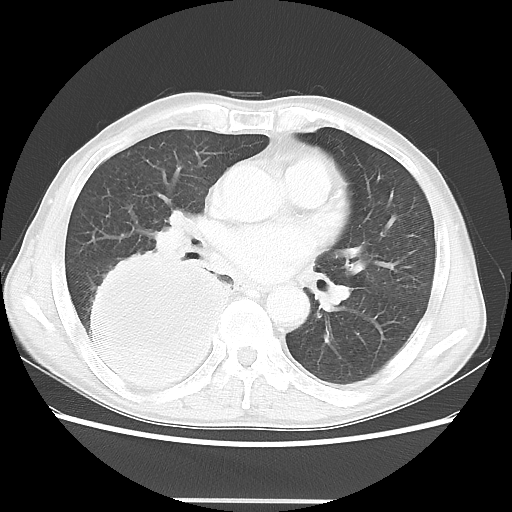
Chest CT, one axial slice; position 23 of 48 along the scan axis; reconstruction kernel LUNG; lung window (W 1500 / L -600 HU); 5 mm slice thickness; 512 × 512 image matrix, field of view 361 × 361 mm. Male patient, age 66 years. From the clinical record (not read from this slice): clinical TNM (as recorded): T4 N1 M1; histopathological grade: G3.
Outlined on this slice (rectangle marked by the reading radiologist):
- lung tumour (recorded histology: small cell carcinoma): bounding box (x1, y1, x2, y2) in pixels: (68, 246, 239, 393)